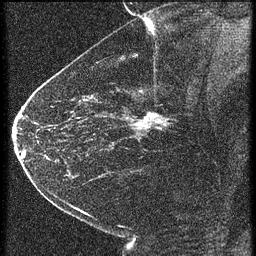
Breast MRI (dynamic contrast-enhanced), one sagittal slice; slice 40 of 60 in the series (ordered by position); 4 images stored at this slice position (order not interpretable as contrast timing); 1.5 T; TE 4.2 ms, TR 21.3 ms; 1.5 mm slice thickness; 256 × 256 image matrix, field of view 180 × 180 mm. Female patient, age 43 years. From the clinical record (not read from this slice): setting: breast cancer imaged before/during neoadjuvant chemotherapy; receptor status: HER2-positive.
Structures marked on this image (semi-automatically segmented with operator editing):
- analysis volume of interest (the breast-tissue region the enhancement analysis was run in; not a lesion): bounding box [x1, y1, x2, y2] px = [122, 100, 187, 151]
- tumour enhancement mask (voxels above the 90 % enhancement threshold inside the analysis volume of interest): [132, 114, 167, 129]